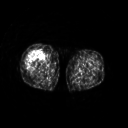
FDG PET of an extremity soft-tissue mass (from a PET/CT study), one axial slice. Position 225 of 311 along the scan axis. 3.27 mm slice thickness. 128 × 128 image matrix, field of view 500 × 500 mm. Female patient, age 57 years. Case-level facts recorded for this patient, not image findings: histological type: pleiomorphic undifferentiated sarcoma; grade: high; site of the primary tumour: right quadricep.
Annotated regions visible in this slice (expert contour drawn on MRI and transferred to this co-registered scan by the dataset authors):
- tumour plus oedema (research contour): bounding box <26,51,42,69> (left, top, right, bottom; pixels)